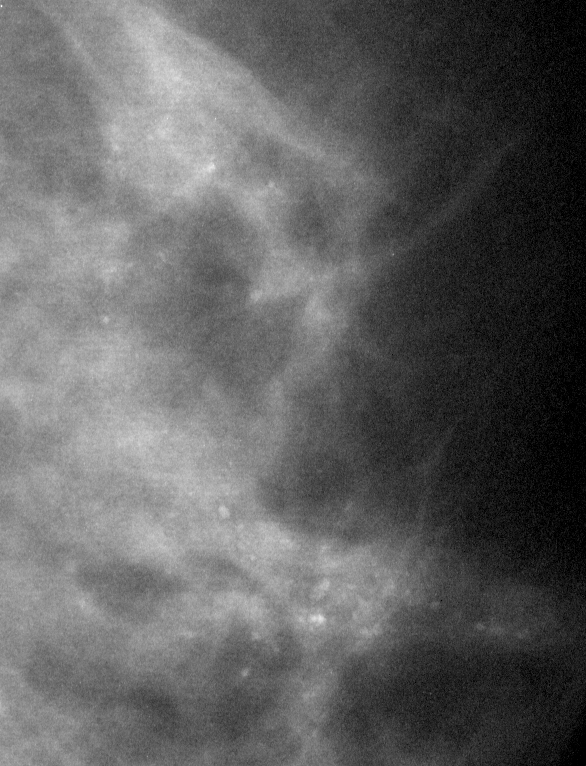
Cropped region of a digitized screen-film mammogram centred on a radiologist-marked abnormality, right breast, MLO view, BI-RADS breast density category 2 (scale 1–4).
- Calcifications, morphology fine linear branching, distribution linear; BI-RADS assessment category 5; subtlety rating 4 on a 1 (subtle) to 5 (obvious) scale; pathology (as recorded): malignant.